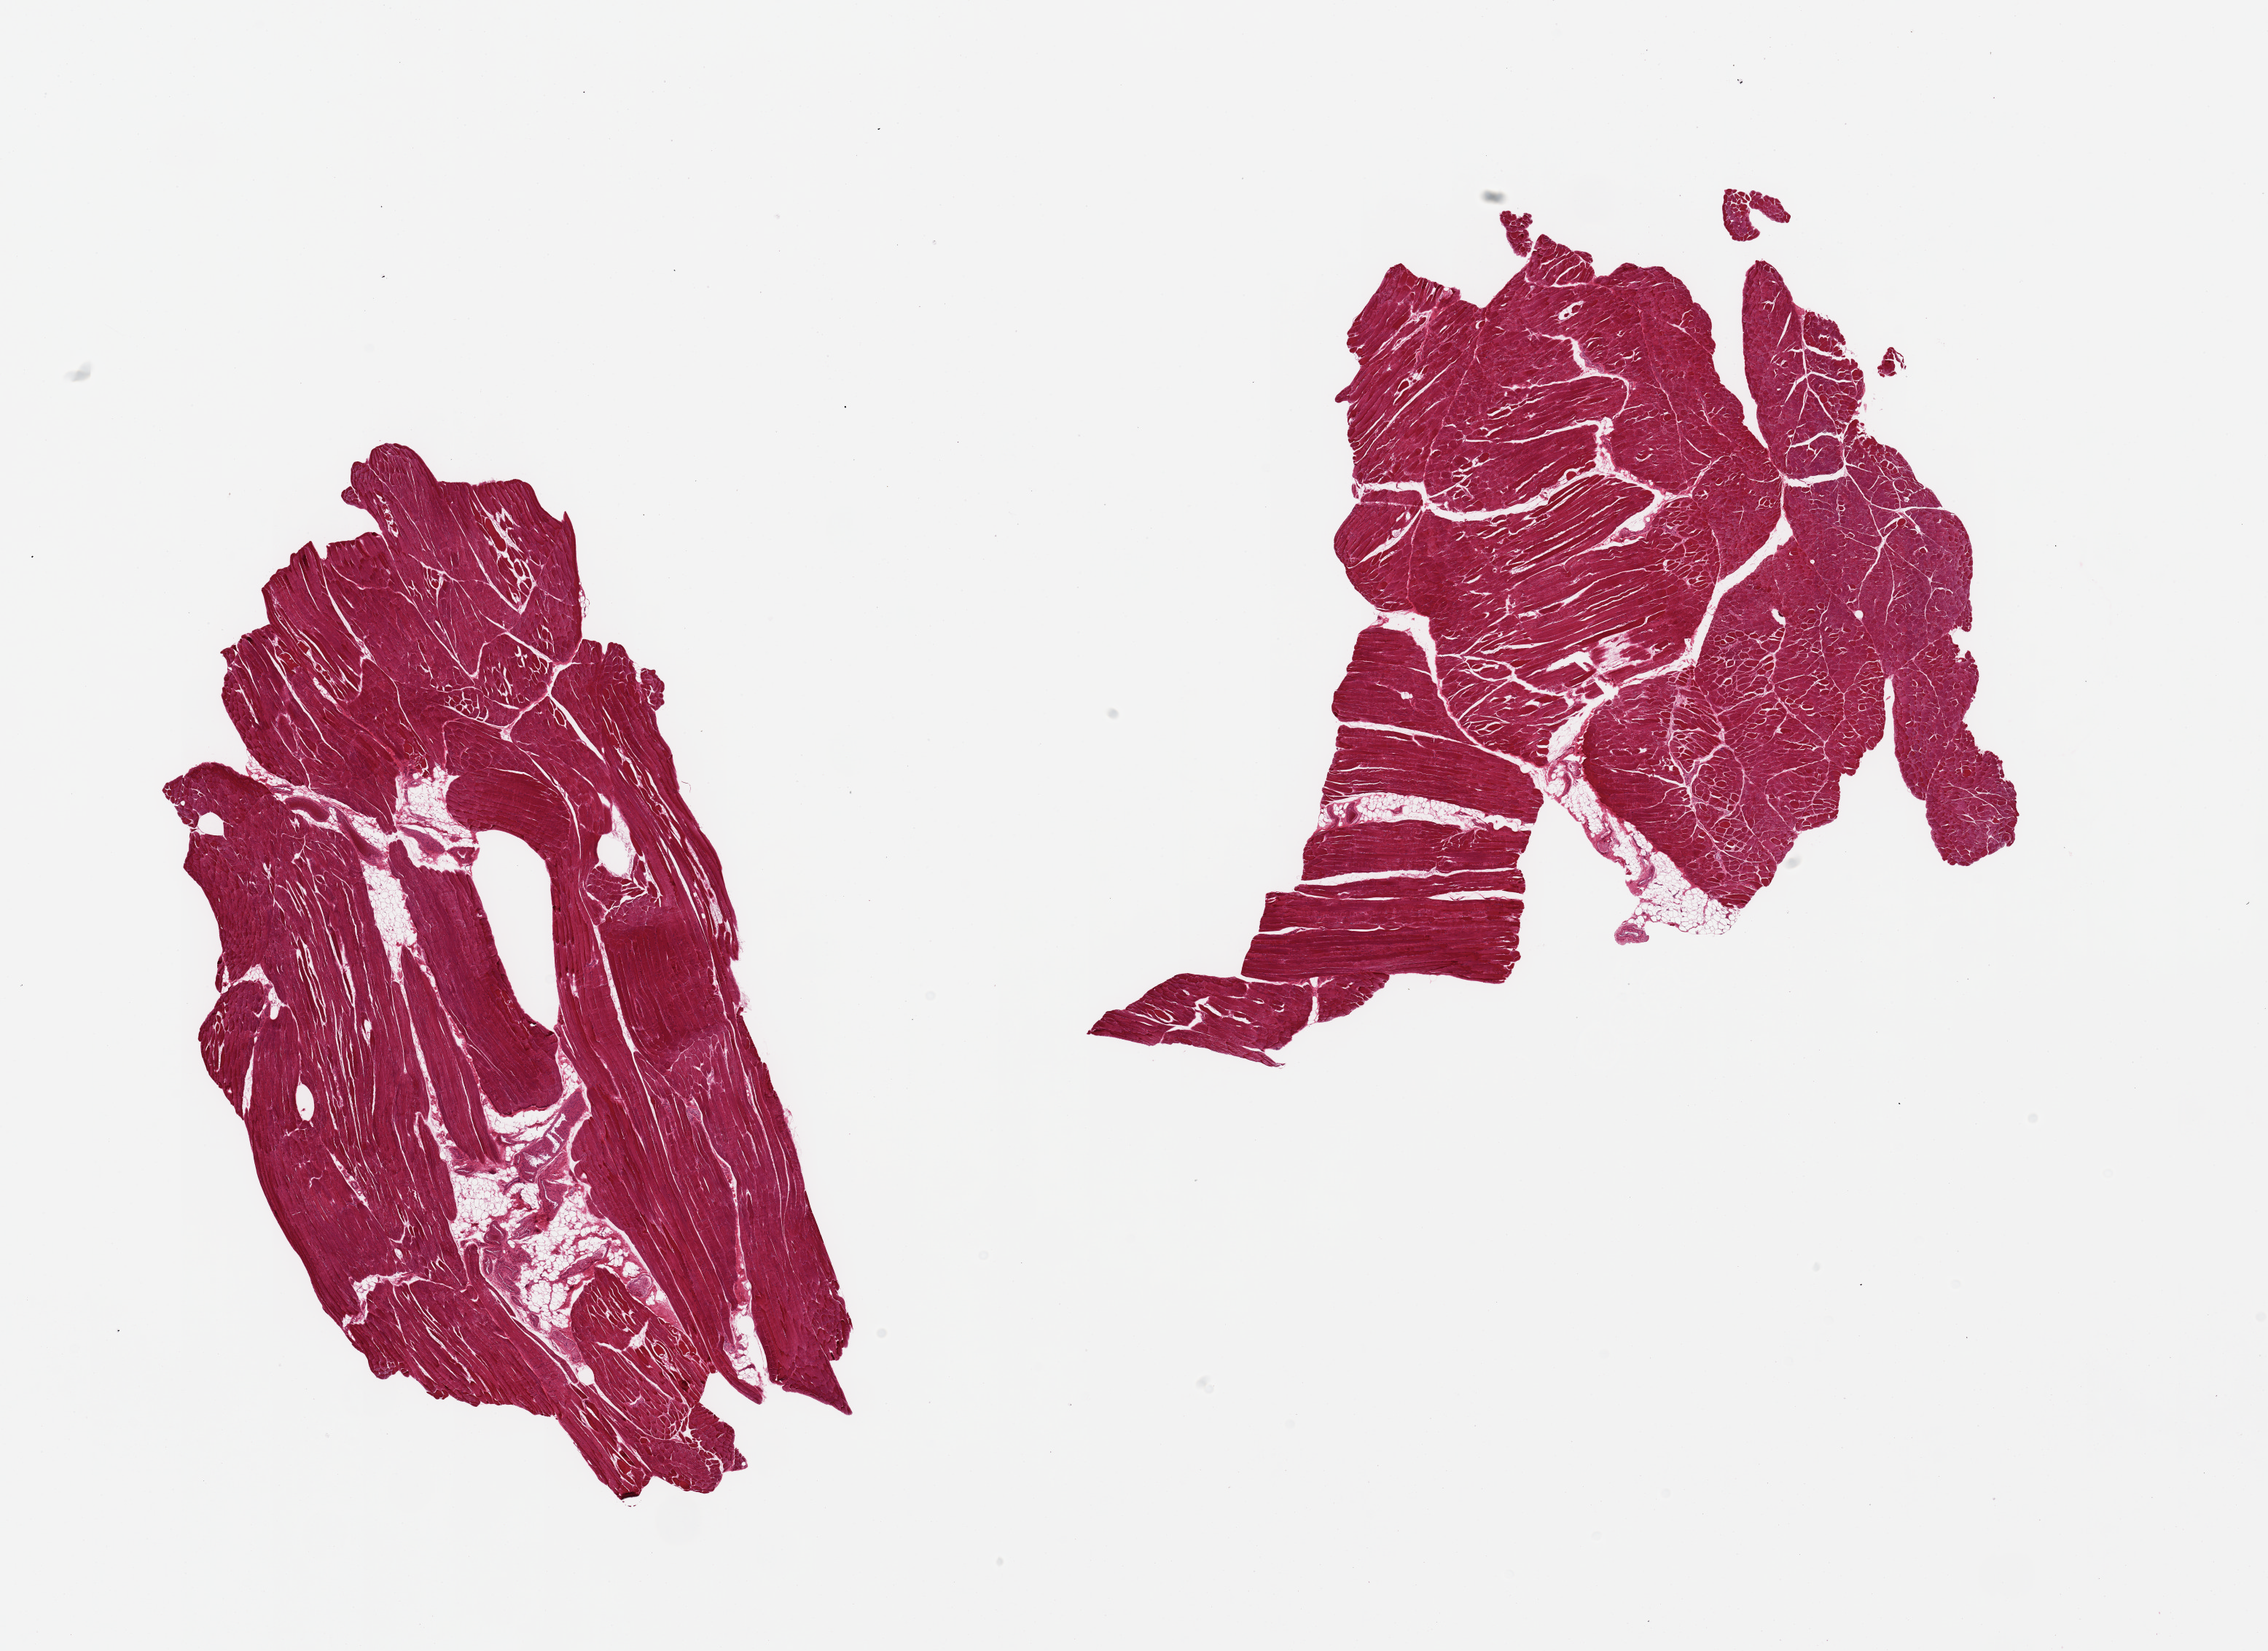
Haematoxylin and eosin whole-slide image, brightfield — a low-resolution overview of the entire scanned area, about 24.6 x 17.9 mm (acquisition: 20x scan). PAXgene-fixed paraffin-embedded (PFPE) section. Section of skeletal muscle (target tissue). Donor tissue sample. Male donor.
• pathologist's review note for this sample: 2 pieces; one piece includes ~10% fat, vessels, and nerve; second has <10% fat